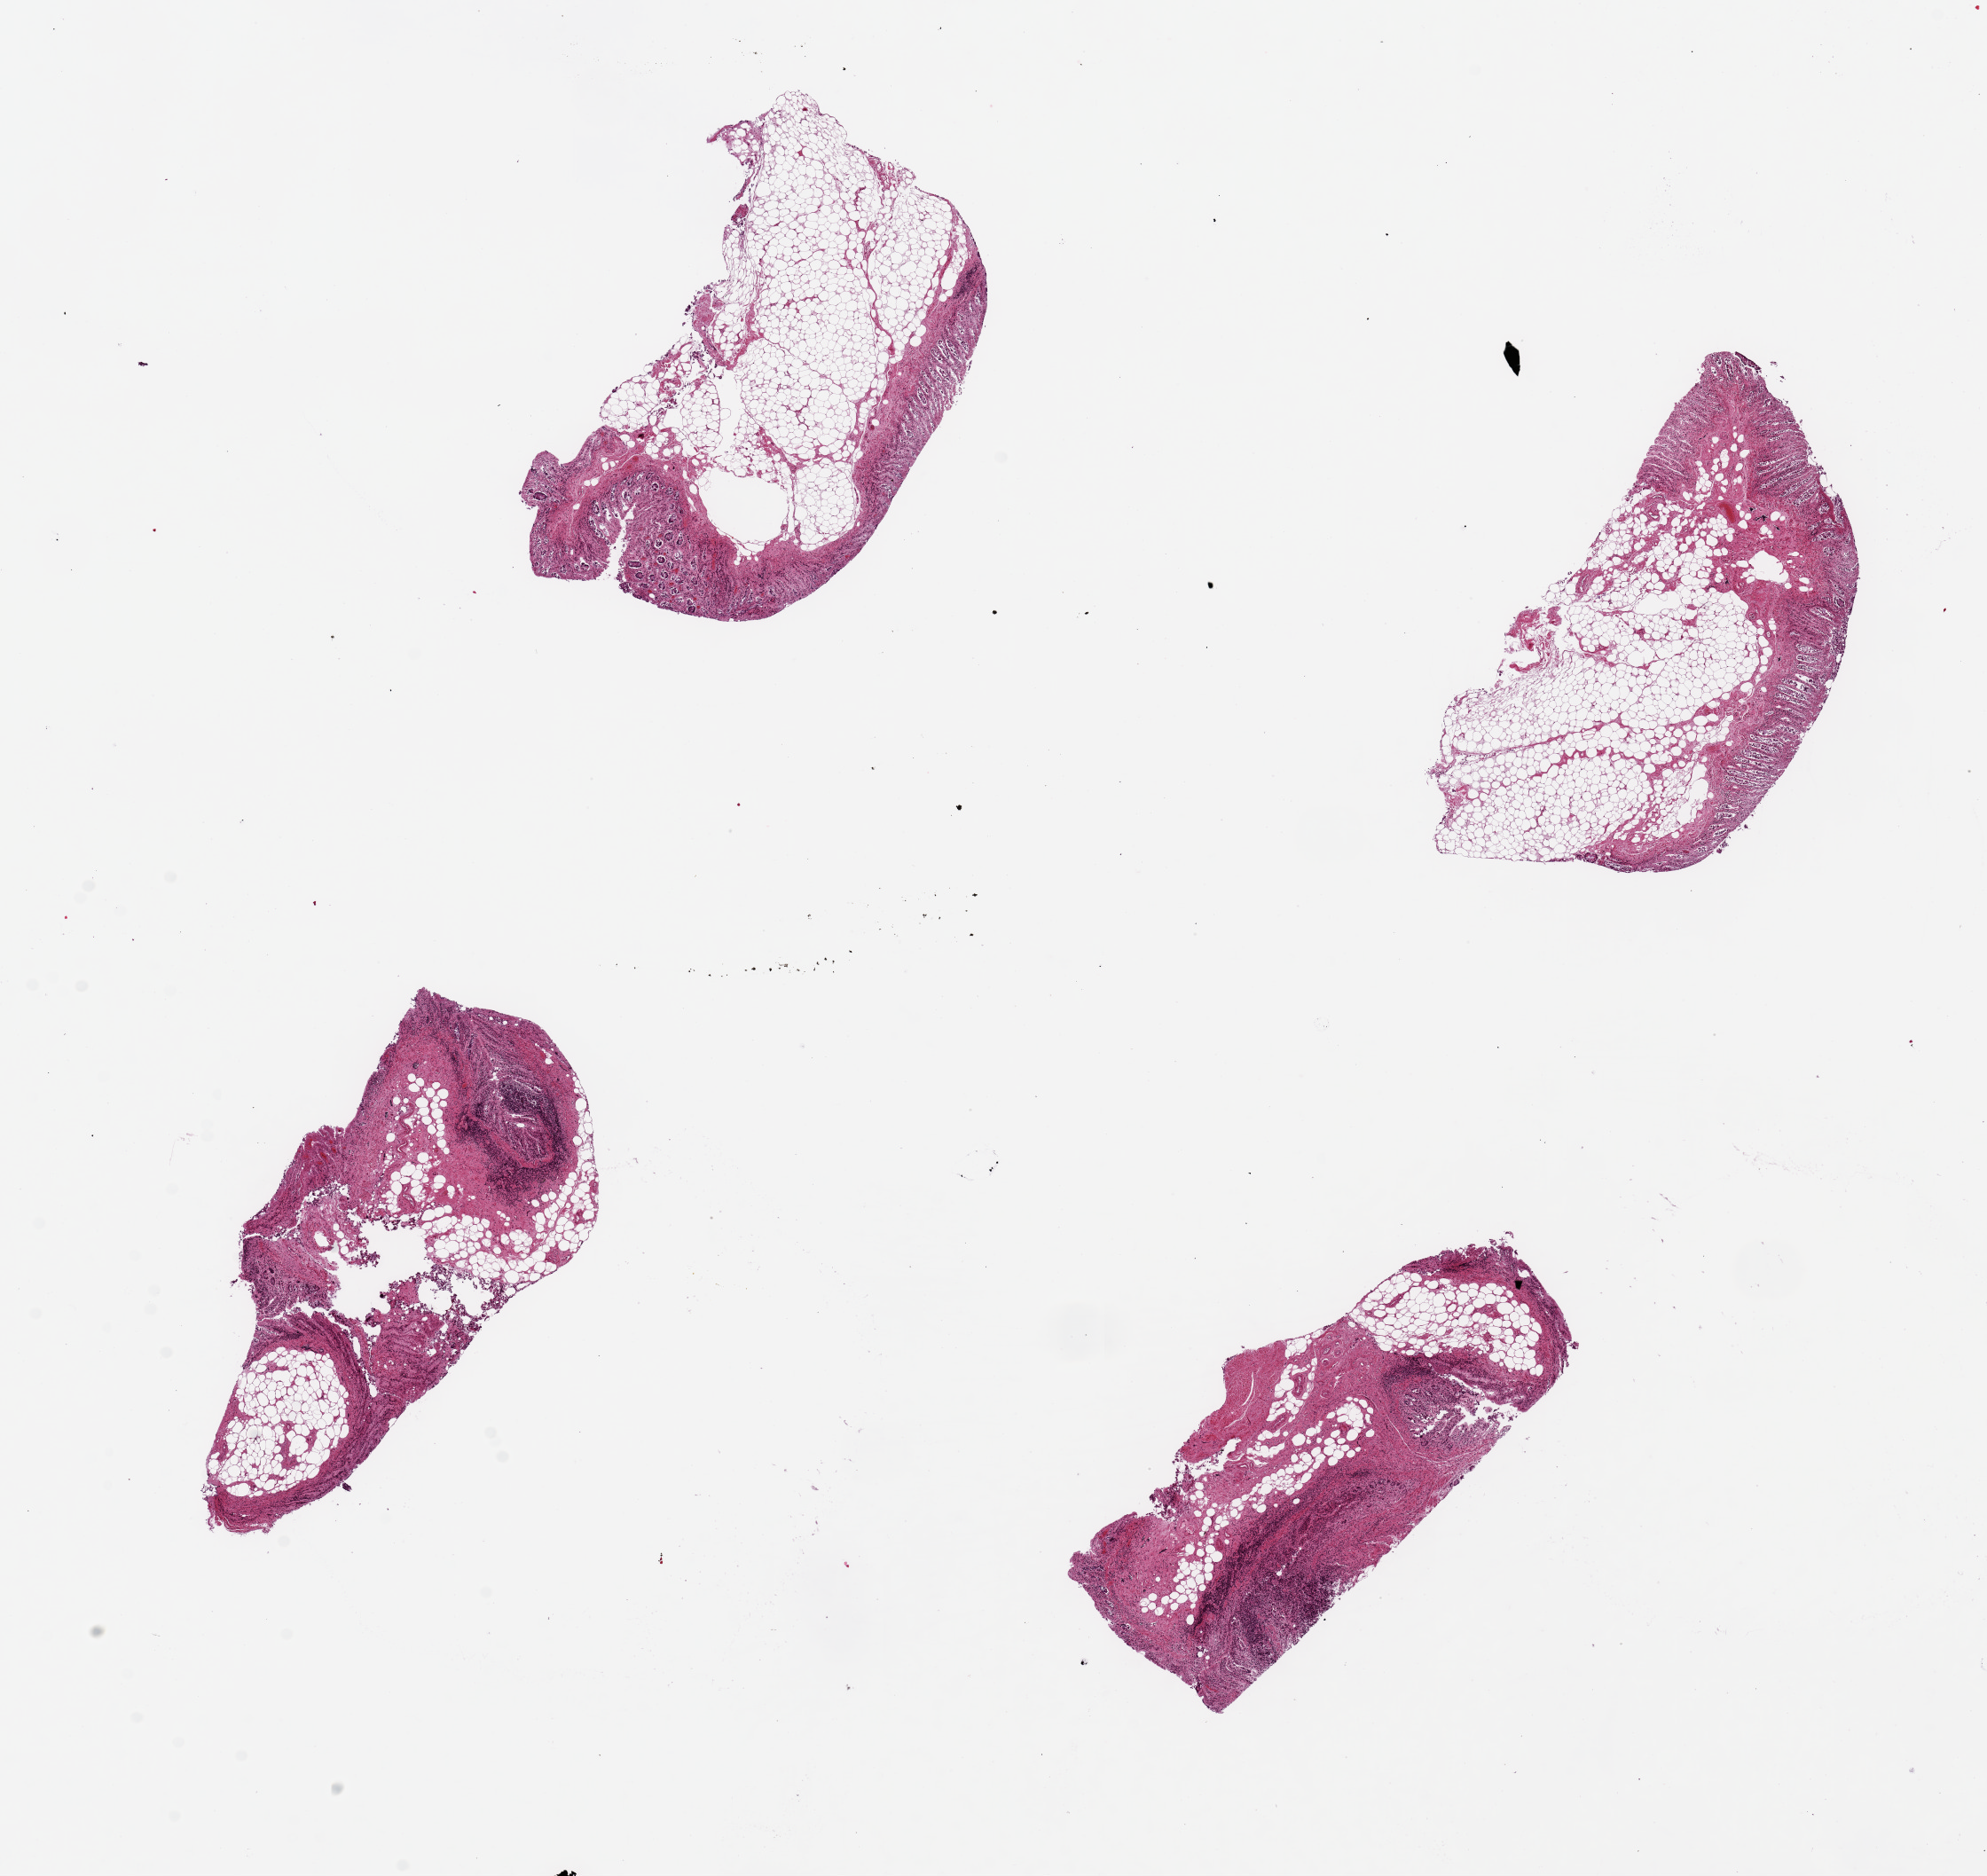
Digitized H&E-stained section, brightfield, a low-resolution overview of the entire scanned area, about 17.7 x 16.7 mm. PAXgene-fixed, paraffin-embedded tissue. Sampled site (target tissue): ileum. Tissue donor sample. Donor: male.
Reviewer comment on this tissue sample: 4 pieces, up to 5x3mm; autolyzed mucosa with small lymphoid groups (marked on image); no muscle (good); lots of submucosal adipose (can't be helped).